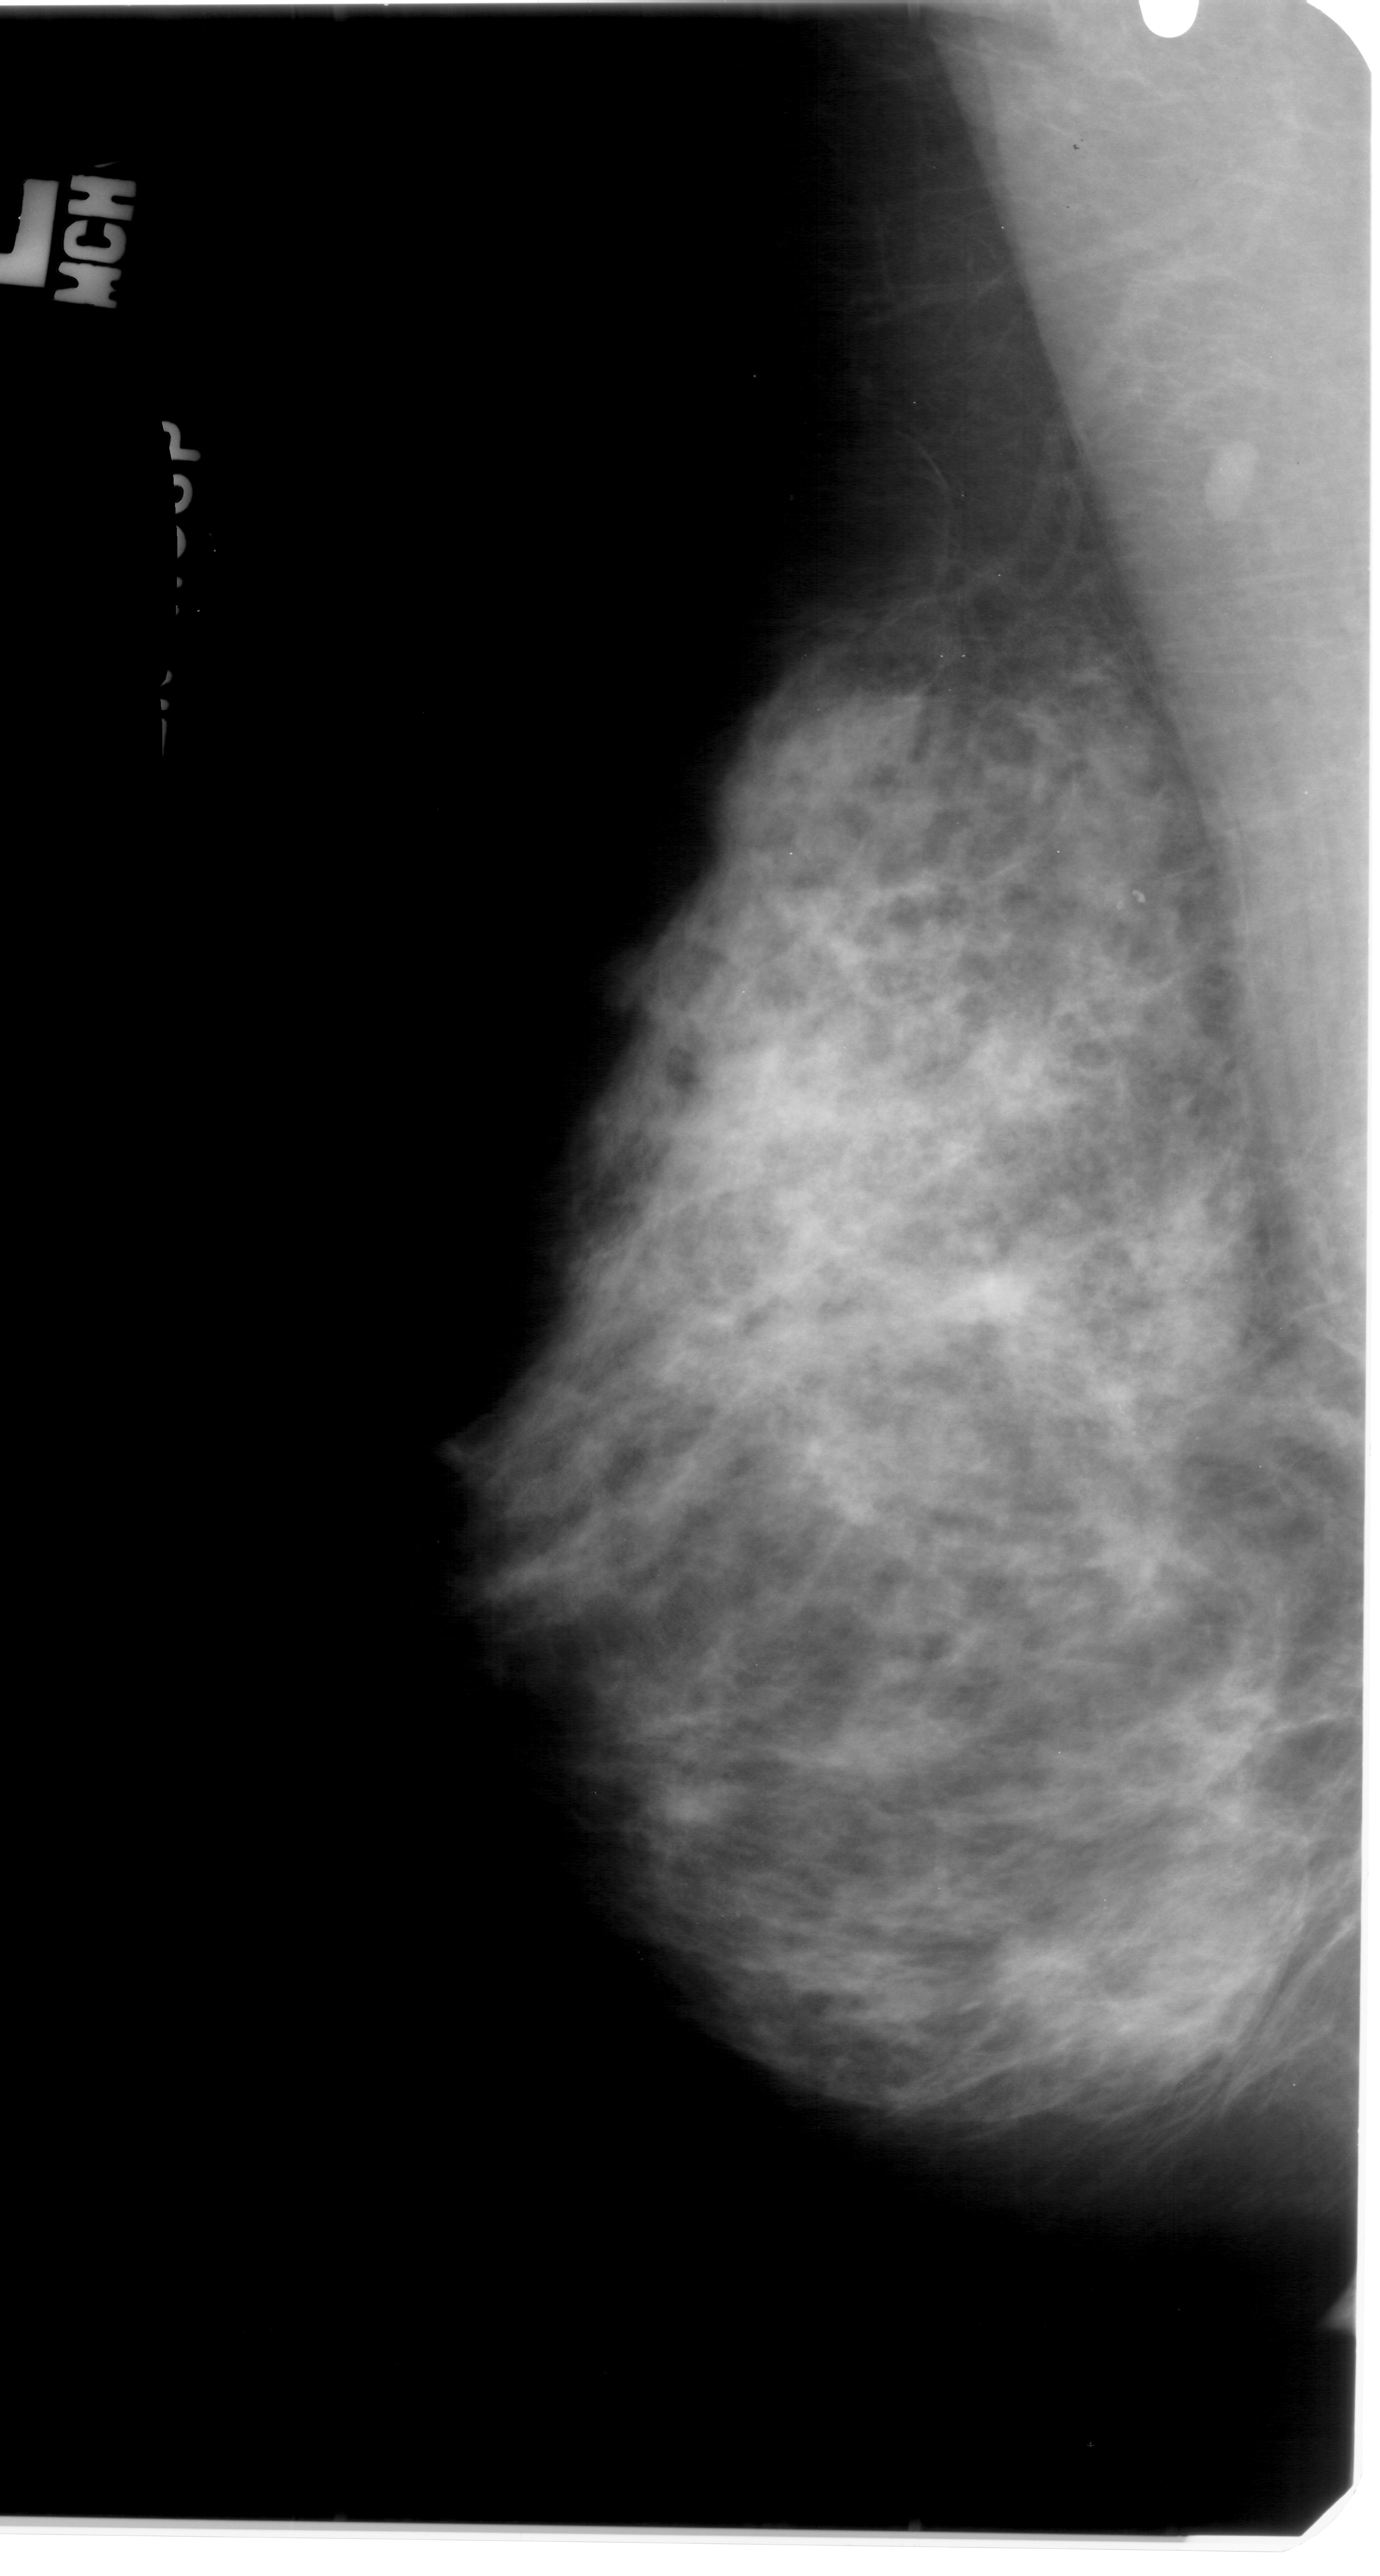
Digitized screen-film mammogram; left breast; mediolateral oblique (MLO) view; BI-RADS breast density category 3 (scale 1–4); 1380 × 2576 image matrix.
Expert-marked regions of interest on this film, with their recorded descriptors:
- calcifications, morphology pleomorphic, distribution clustered; BI-RADS assessment category 4; pathology result (as recorded, not read from the image): benign: box from (x=1093, y=1375) to (x=1234, y=1467) px